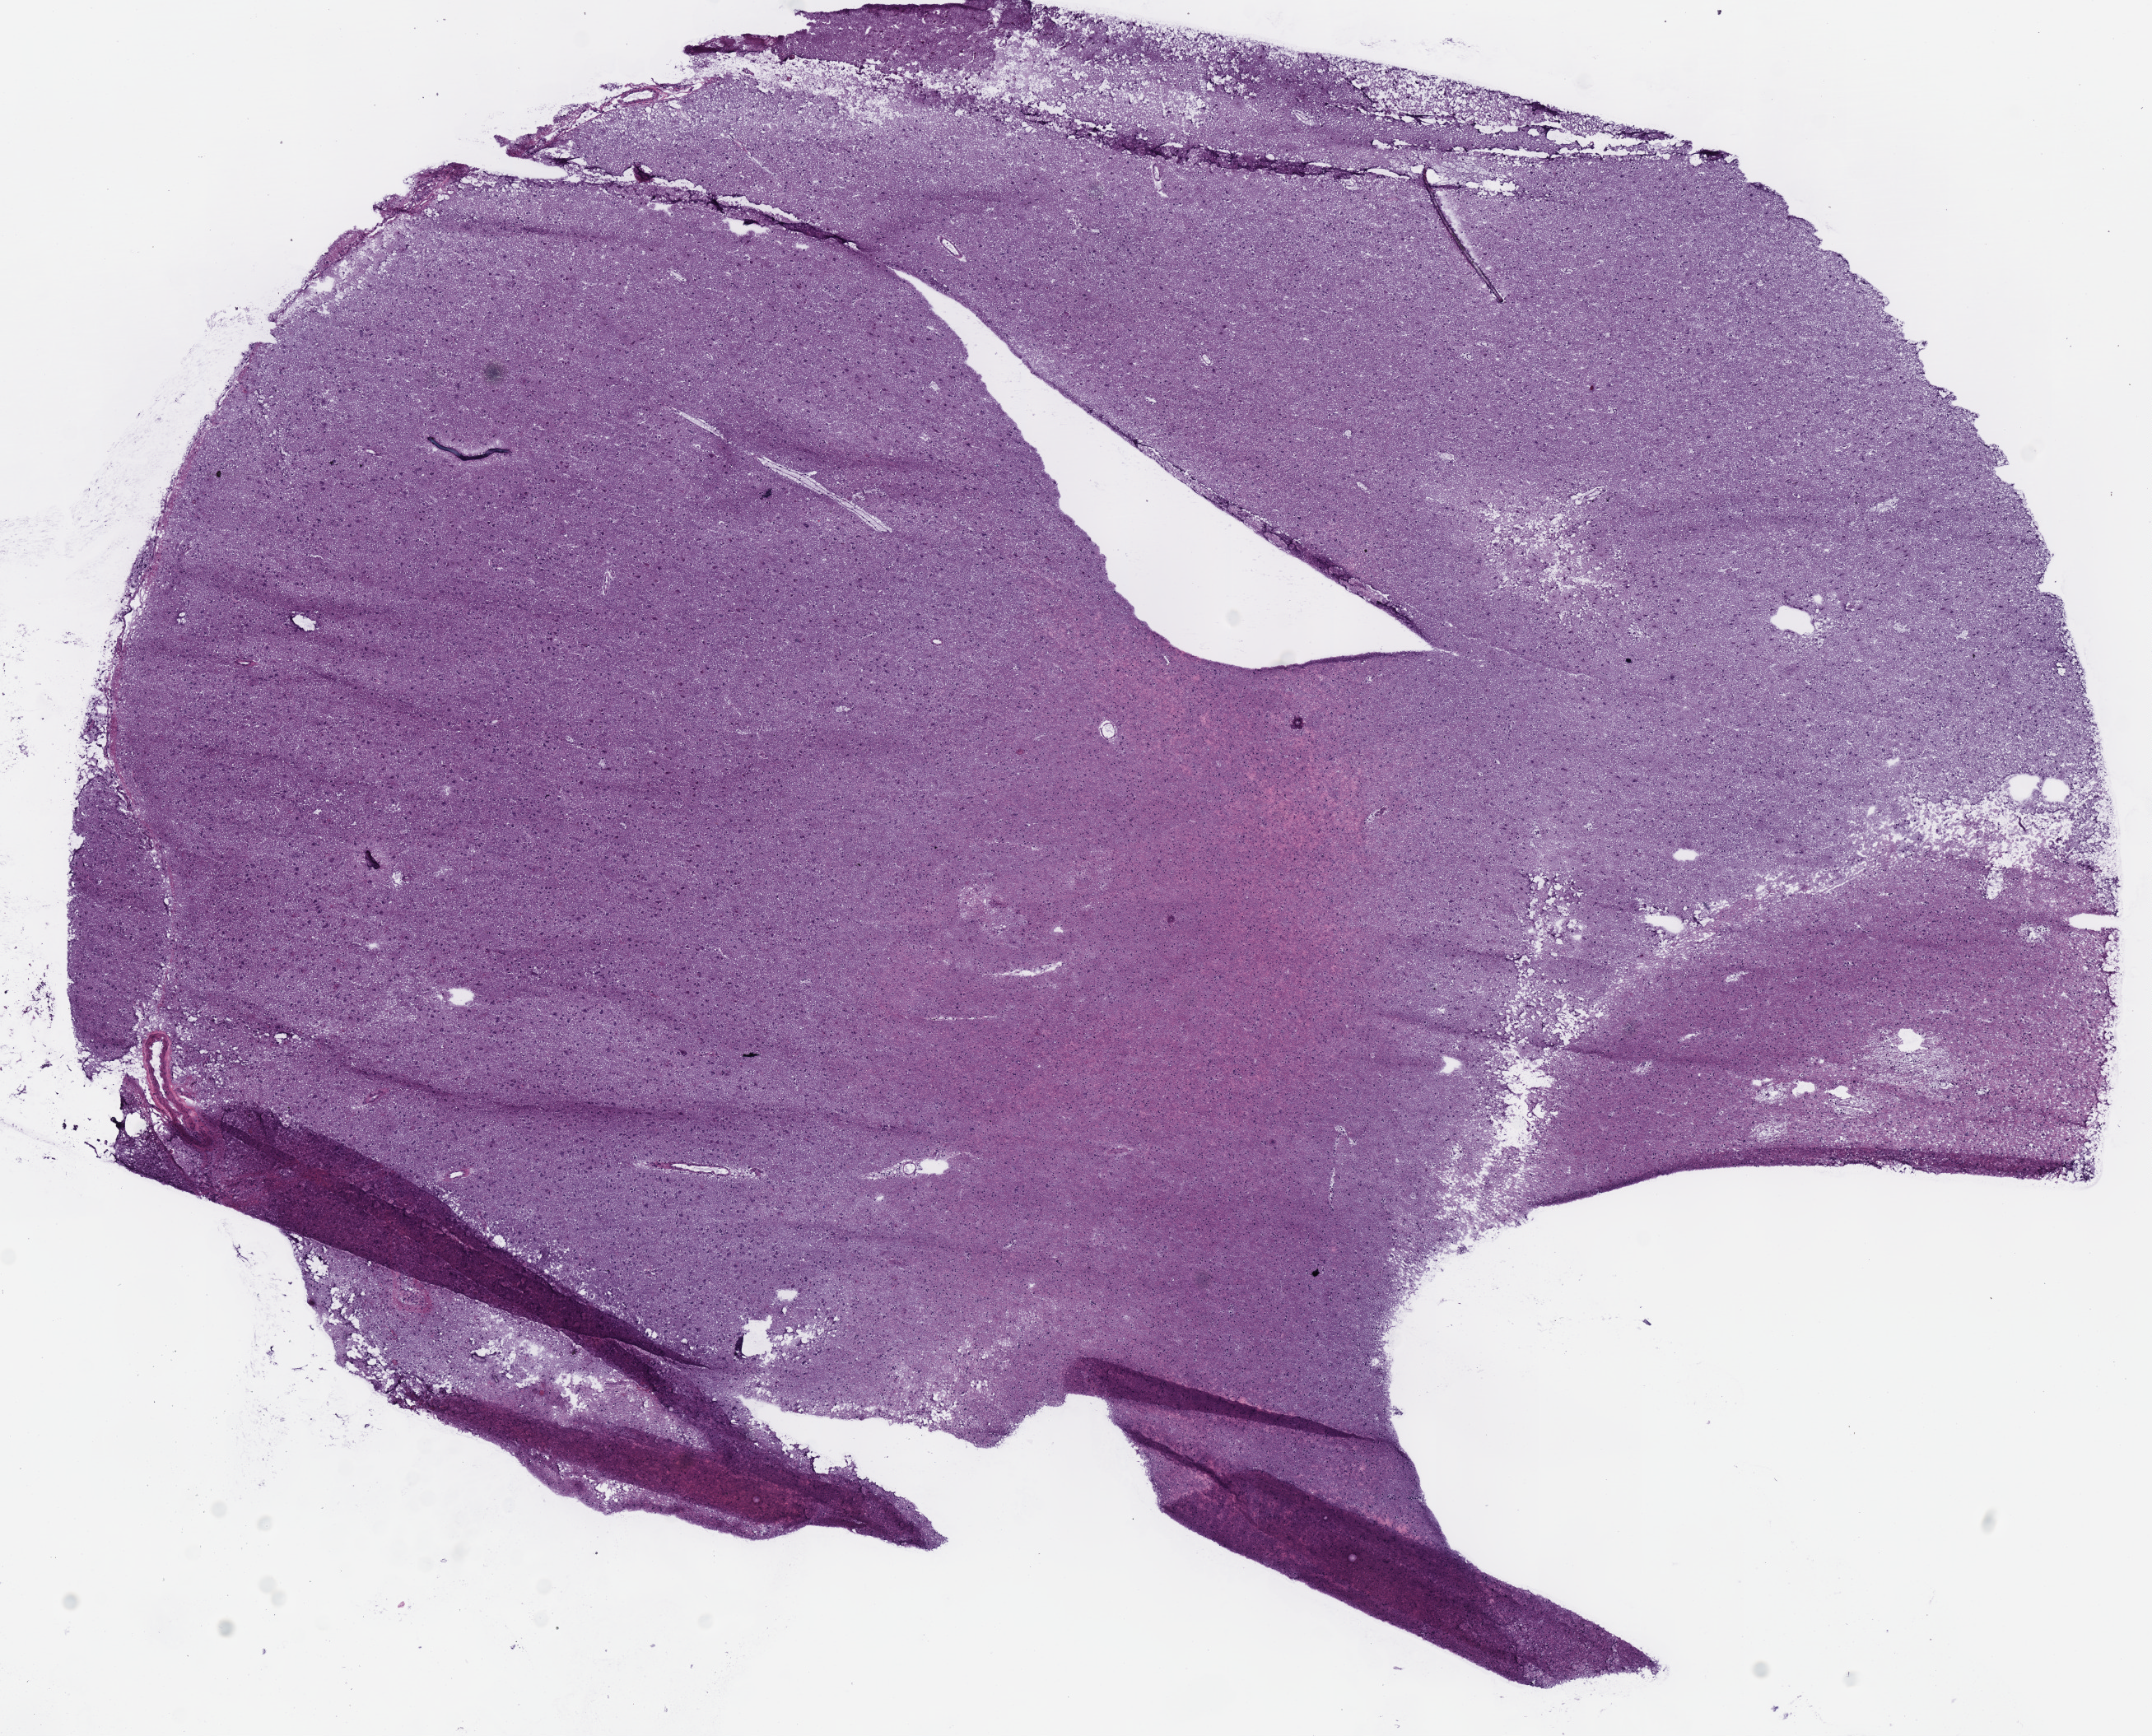
Whole-slide histology image, H&E-stained — shown as a low-resolution overview of the whole scanned area (about 10.3 x 8.3 mm, acquisition: 40x scan); frozen section; brain, primary tumour sample. Female, age 61 years at initial diagnosis. Histologic grade: G3 (poorly differentiated). Pathologist review of this section (percent, as recorded): tumour cells 100%, tumour nuclei 60%, normal cells 0%, stromal cells 0%, necrosis 0%.
* diagnosis: Mixed glioma (cerebrum)
* laterality: right